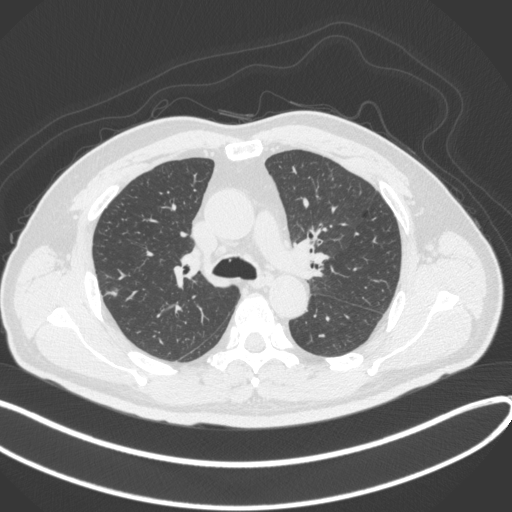
Chest CT, one axial slice; position 227 of 373 along the scan axis; reconstruction kernel B31f; 120 kVp; lung window (W 1500 / L -600 HU); 1 mm slice thickness; 512 × 512 image matrix. Patient: male, 60 years. From the clinical record (not read from this slice): clinical TNM (as recorded): T1c N0 M0.
Structures marked on this image (rectangle marked by the reading radiologist):
- lung tumour (recorded histology: adenocarcinoma): bounding box (x1, y1, x2, y2) in pixels: (98, 282, 120, 301)